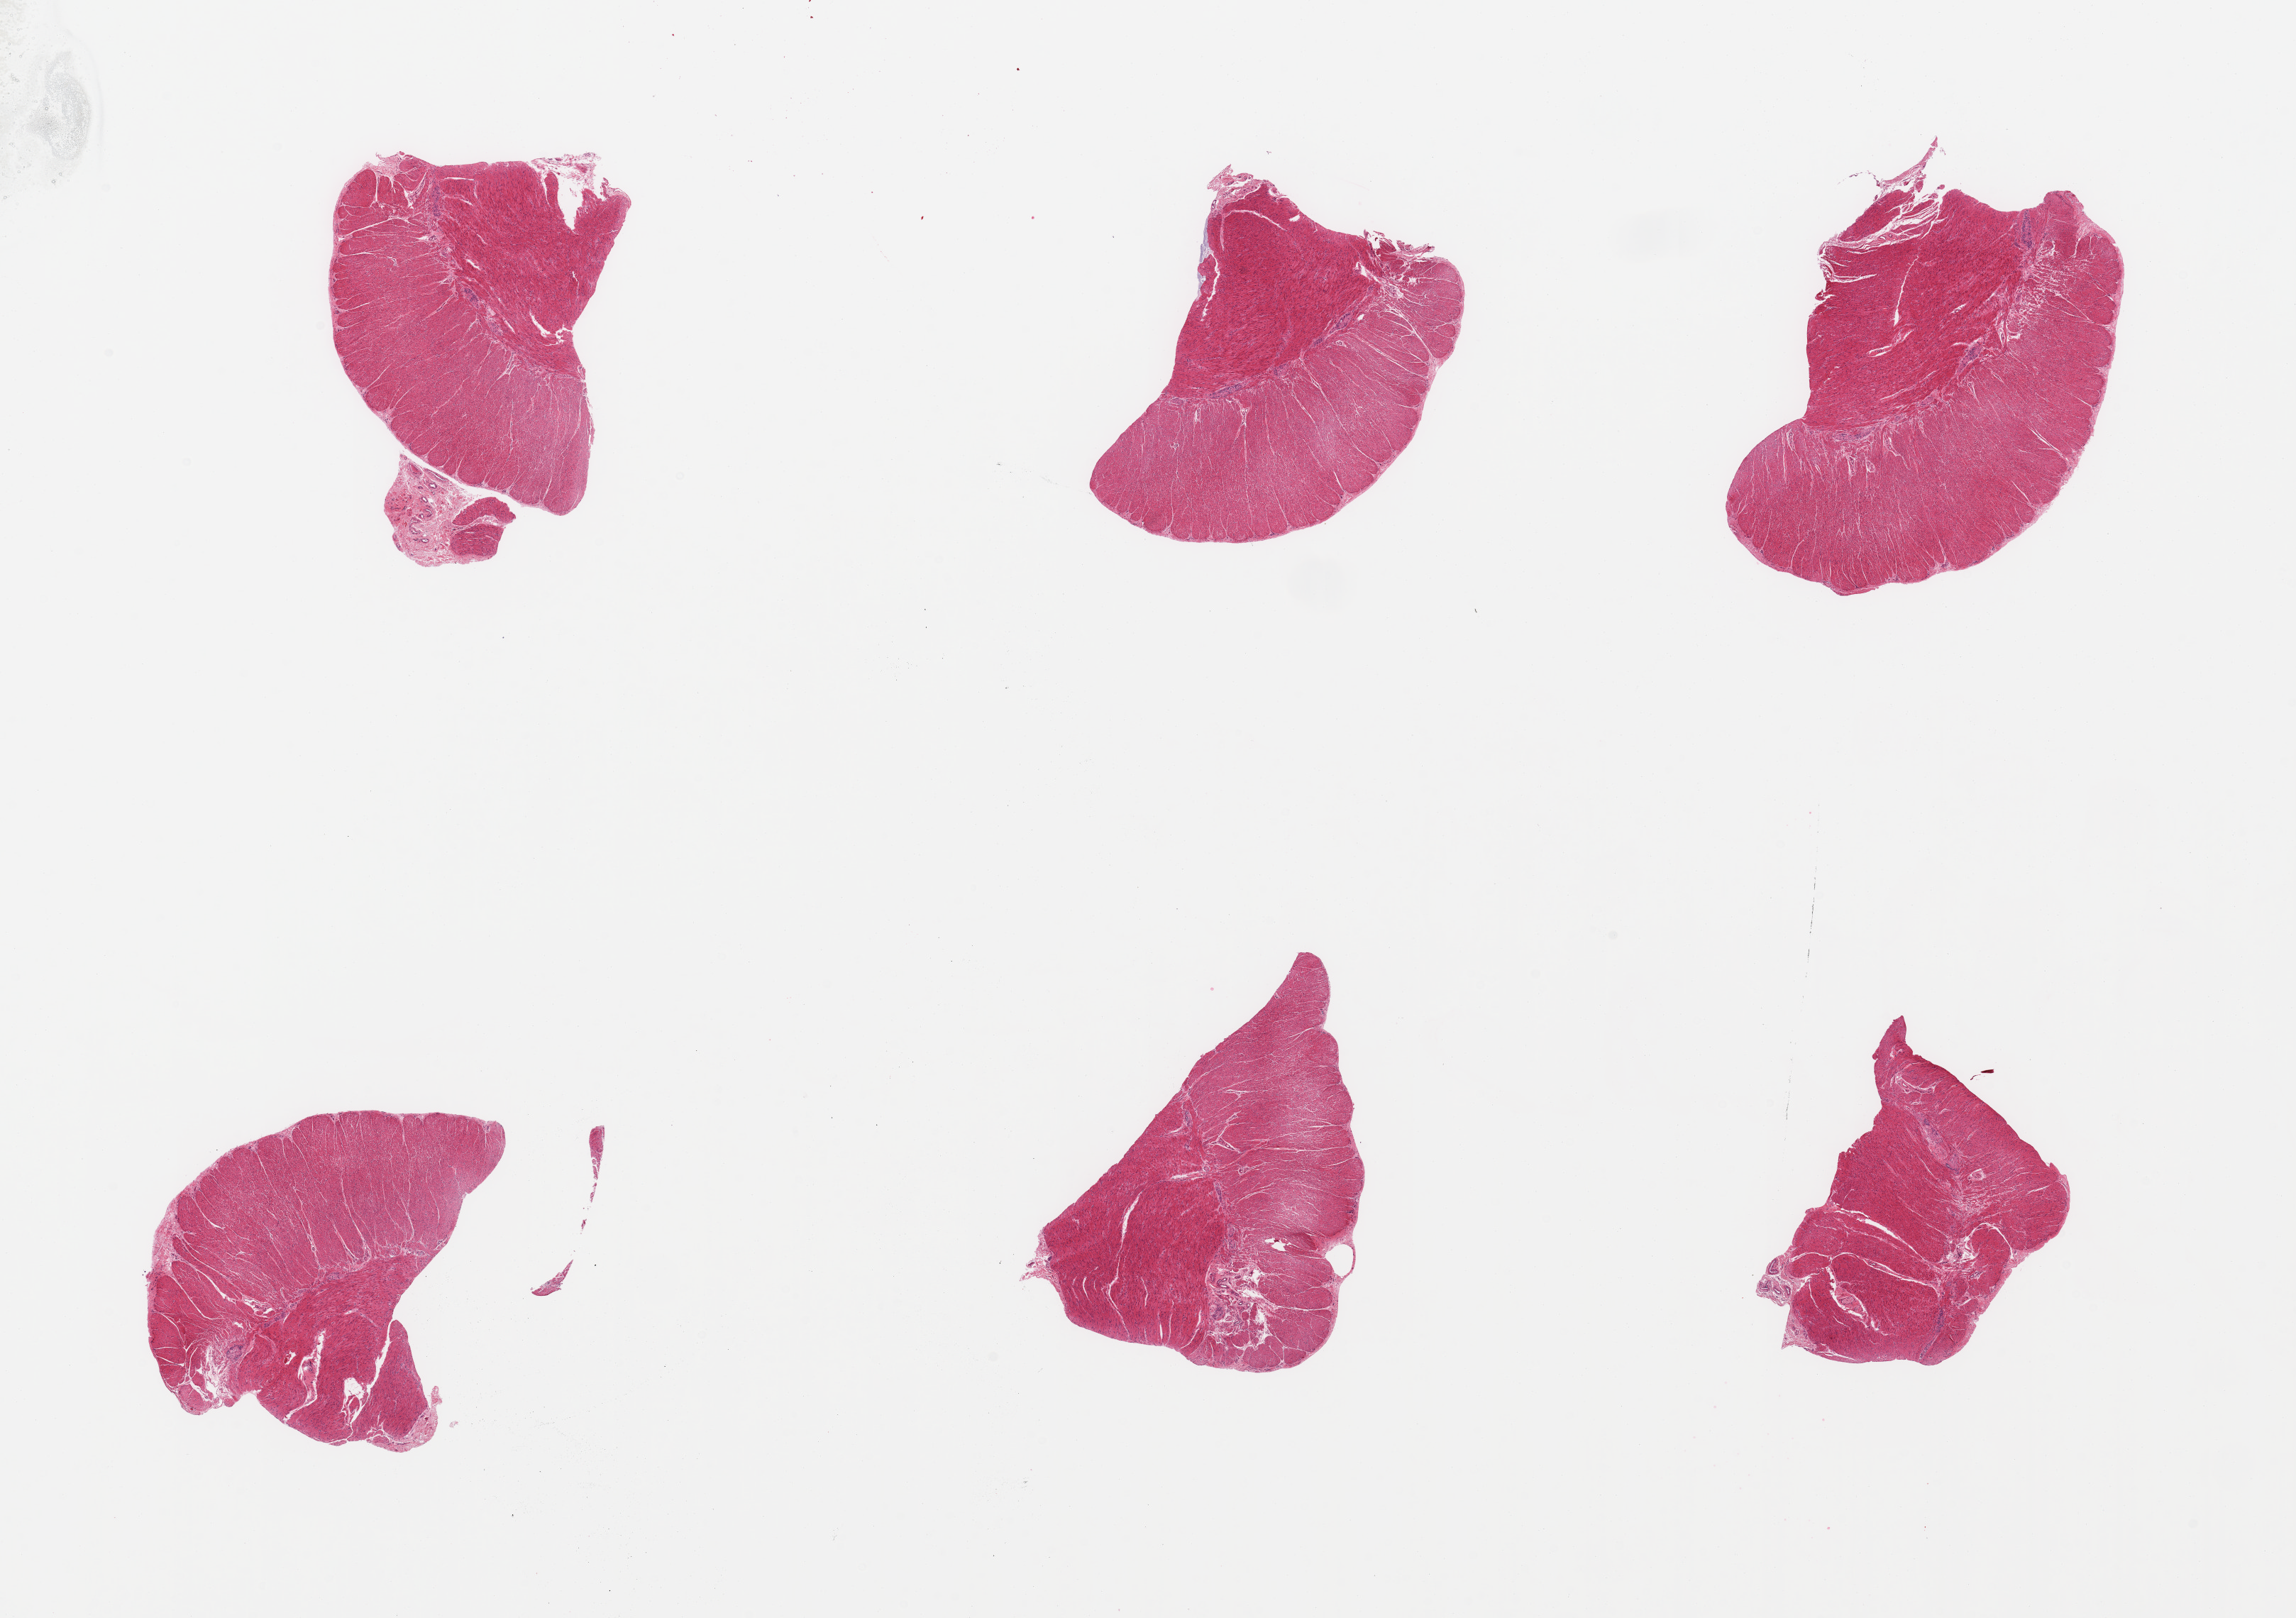
Digitized H&E-stained section — shown as a low-resolution overview of the whole scanned area (about 25.6 x 18.0 mm, slide scanned at 20x); PAXgene-fixed paraffin-embedded (PFPE) section; section of ileum (target tissue); tissue donor sample. Donor: female.
Reviewer comment on this tissue sample: 6 pieces, muscularis, no target mucosa or lymphoid aggregates.